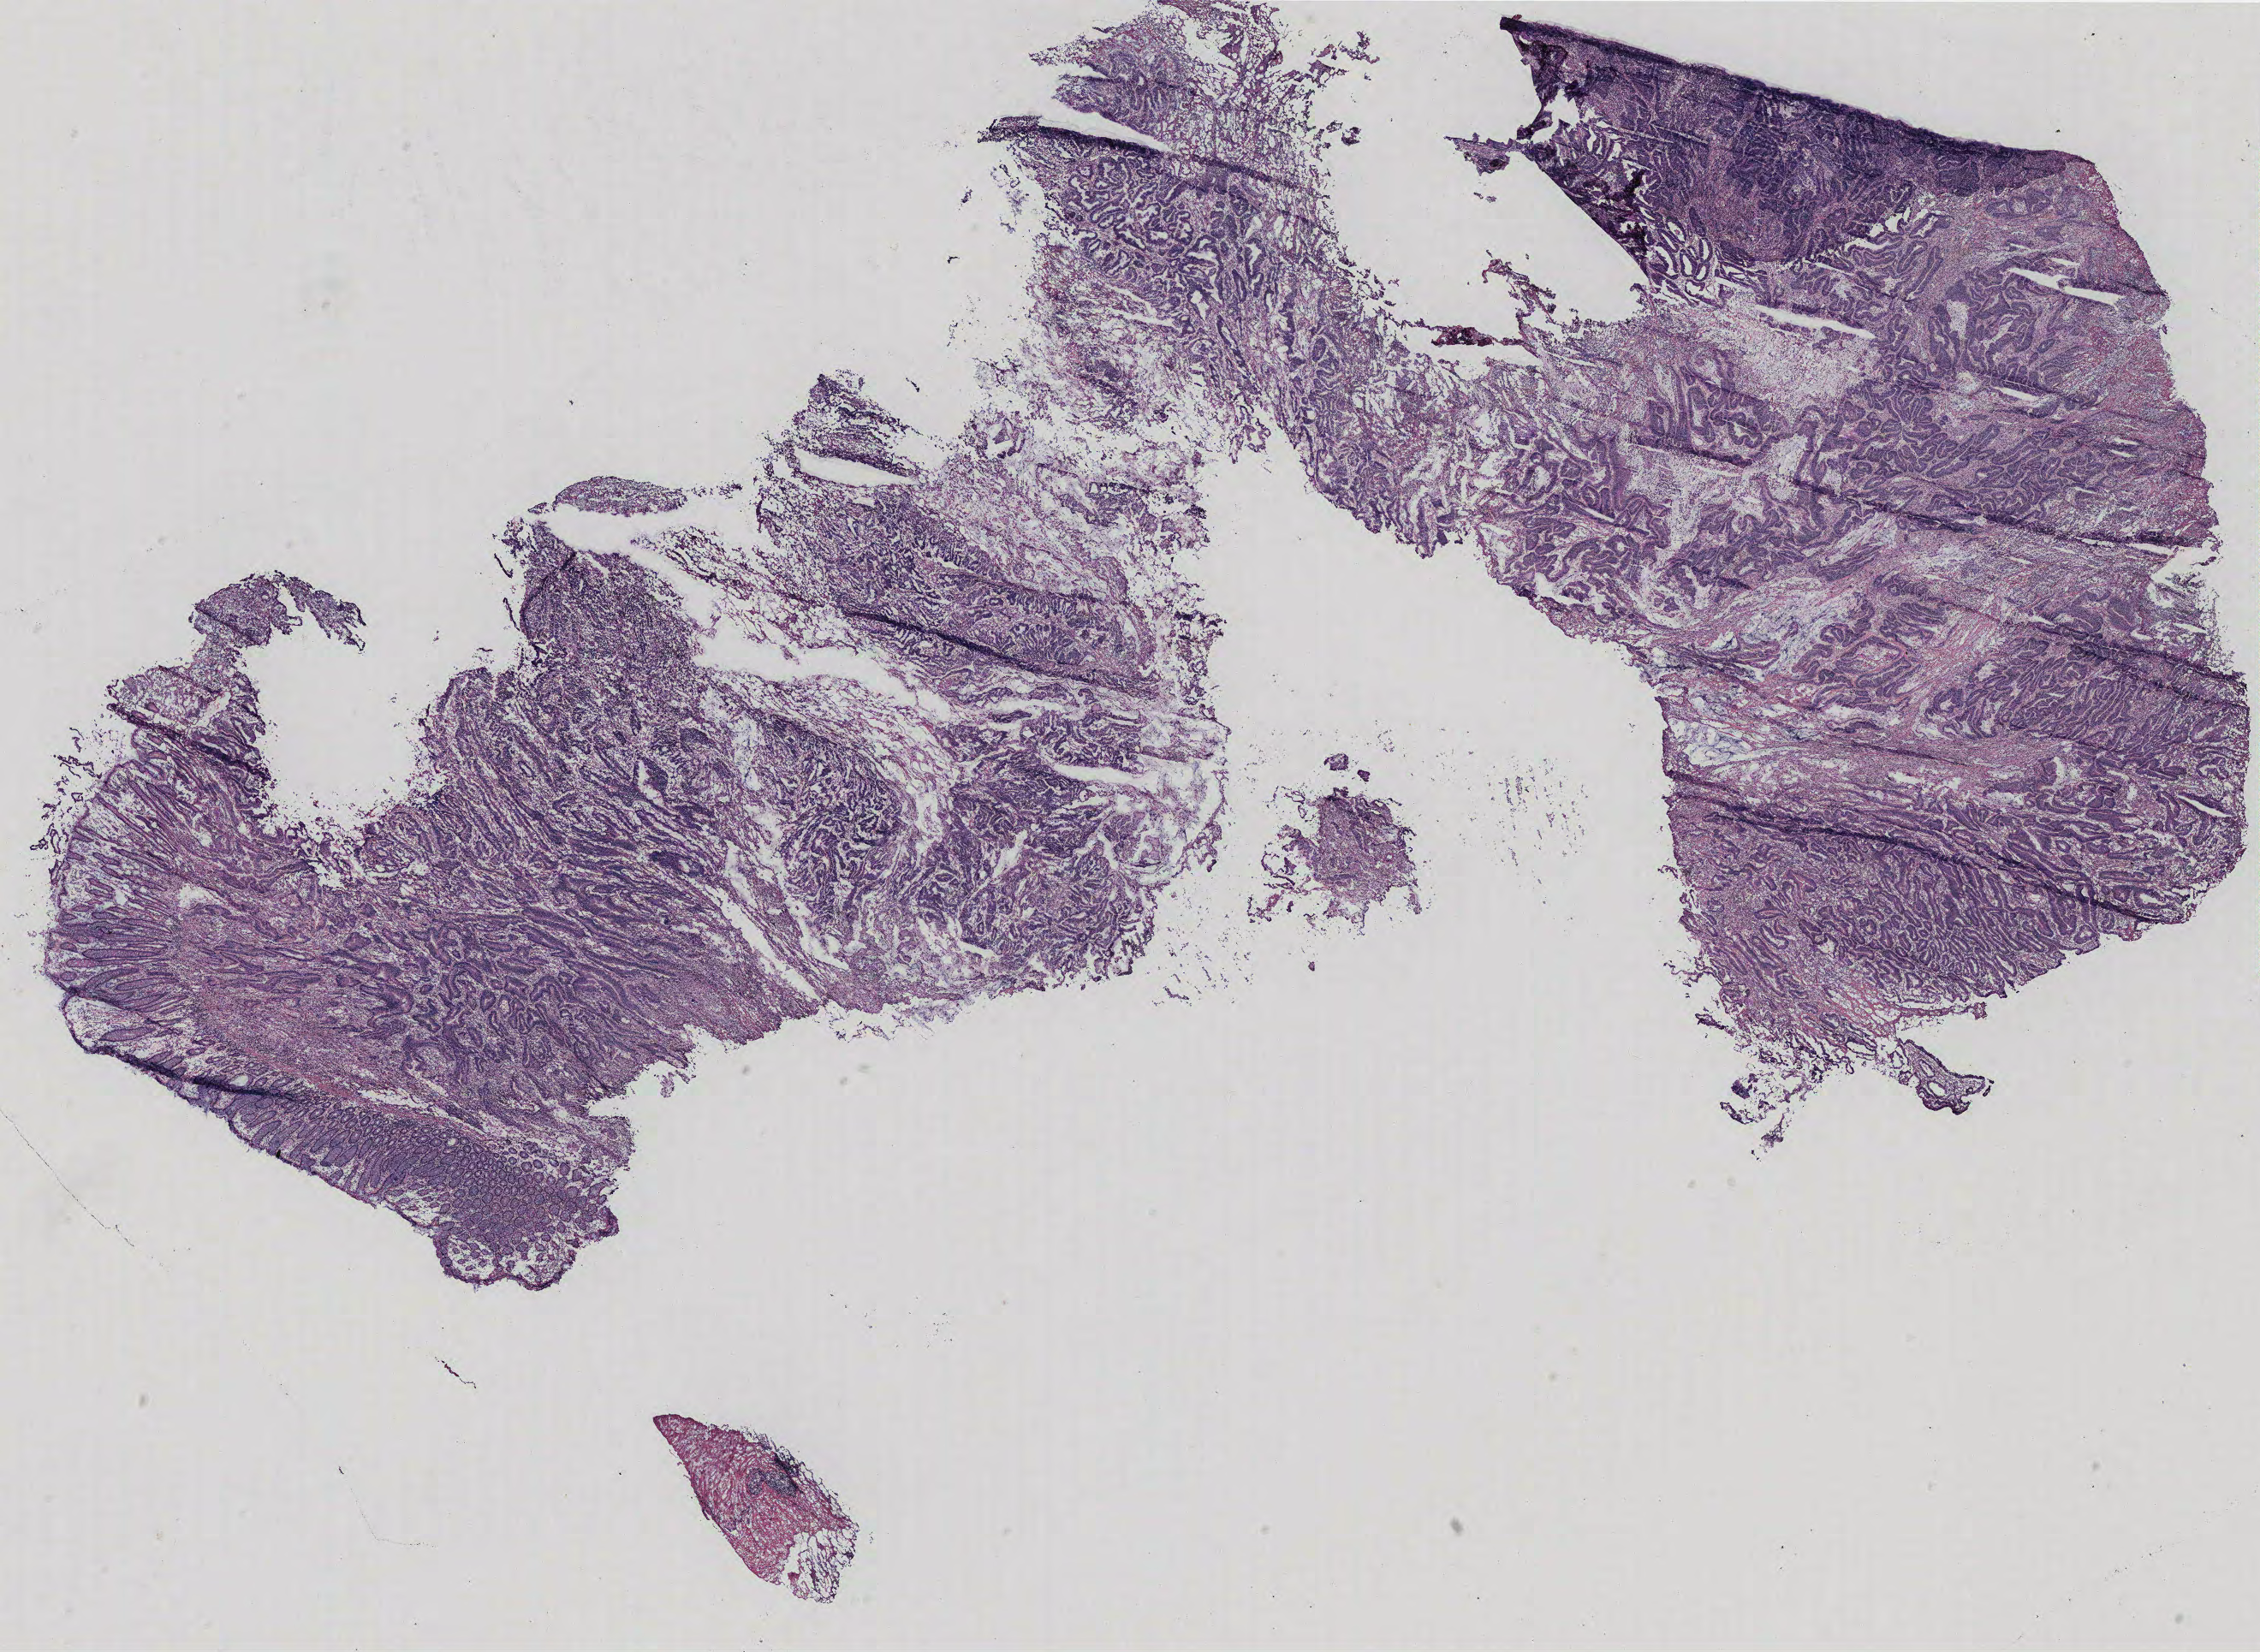
Digitized H&E tissue section (whole slide) — low-resolution overview of the scanned area, about 21.1 x 15.4 mm, colon, tumour tissue. Male, 54 y/o.
Histologic diagnosis: Adenocarcinoma, NOS. AJCC pathologic stage: IIA. Primary tumour site (as recorded): colon.